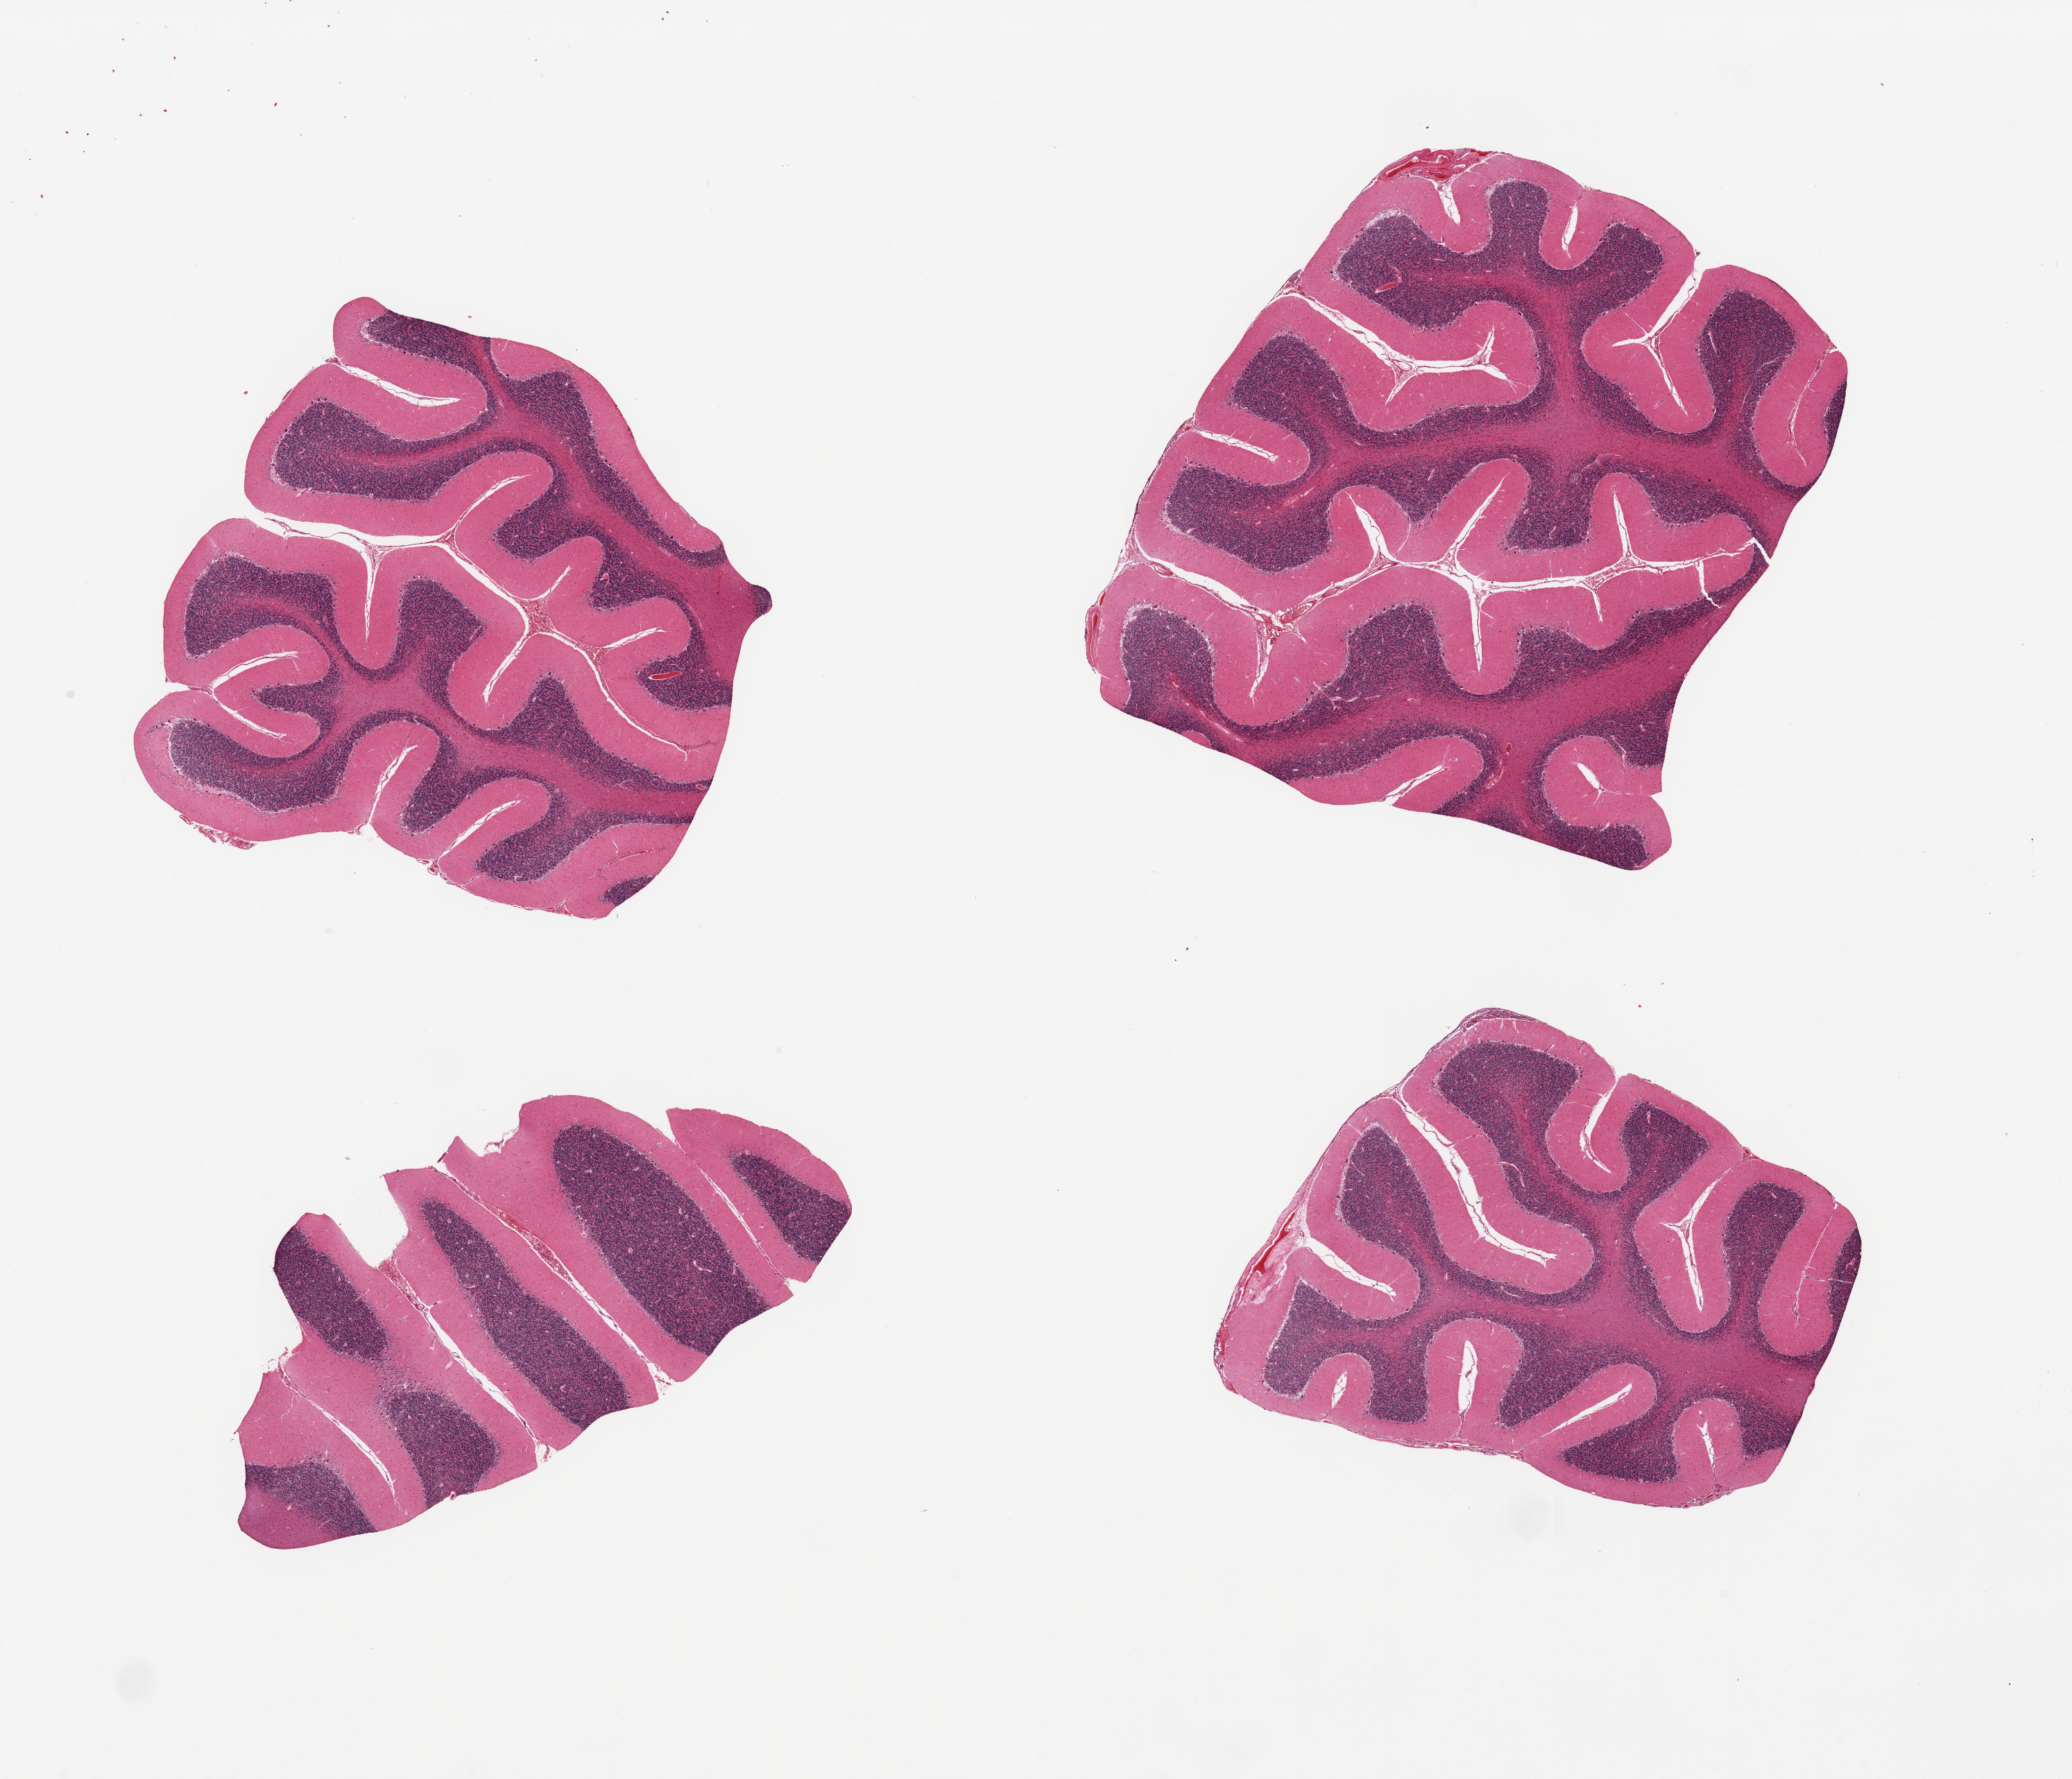
Hematoxylin and eosin (H&E) whole-slide image, a low-resolution overview of the entire scanned area, about 23.6 x 20.3 mm (slide scanned at 20x). PAXgene-fixed paraffin-embedded (PFPE) section. Section of cerebellum (target tissue). Tissue donor sample. Donor: male.
Reviewer comment on this tissue sample: 4 pieces.